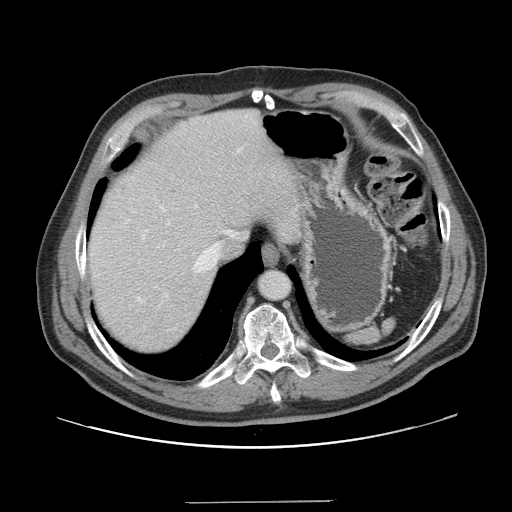
Contrast-enhanced abdominal CT, one axial slice. Position 130 of 151 along the scan axis. 120 kVp. Intravenous contrast given. Soft-tissue window (W 400 / L 40 HU). 2.5 mm slice thickness. 512 × 512 image matrix, field of view 399 × 399 mm. Male patient, age 63 years. Case-level facts recorded for this patient, not image findings: diagnosis: colorectal cancer liver metastases, imaged before liver resection; multiple liver metastases: no; largest metastasis: 2.1 cm.
Annotated regions visible in this slice (manually delineated by an expert):
- hepatic veins: box from (x=143, y=150) to (x=240, y=272) px
- liver: (x=88, y=110)–(x=304, y=355)
- planned liver remnant (the part of the liver to remain after resection): (x=88, y=123)–(x=248, y=355)